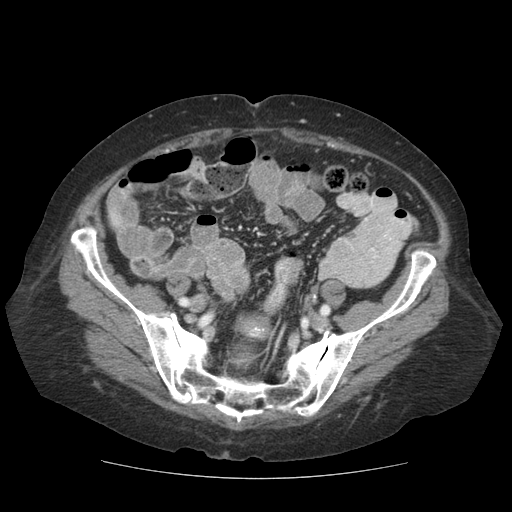
Contrast-enhanced abdominal CT (liver protocol), one axial slice; position 11 of 111 along the scan axis; reconstruction kernel STANDARD; 140 kVp; soft-tissue window (W 400 / L 40 HU); 2.5 mm slice thickness; 512 × 512 image matrix, field of view 360 × 360 mm. Case-level facts recorded for this patient, not image findings: diagnosis: hepatocellular carcinoma (patient treated with transarterial chemoembolisation; whether this scan precedes or follows treatment is not stated here); TNM stage (as recorded): Stage-I; Child-Pugh class: A; tumour differentiation: moderately-poorly differentiated; tumour nodularity: uninodular.
Annotated regions visible in this slice (semi-automatically segmented with operator editing):
- liver parenchyma outside the tumour (the mass and vessels are separate outlines, so this box may not span the whole liver): bounding box [x1, y1, x2, y2] px = [115, 224, 126, 243]